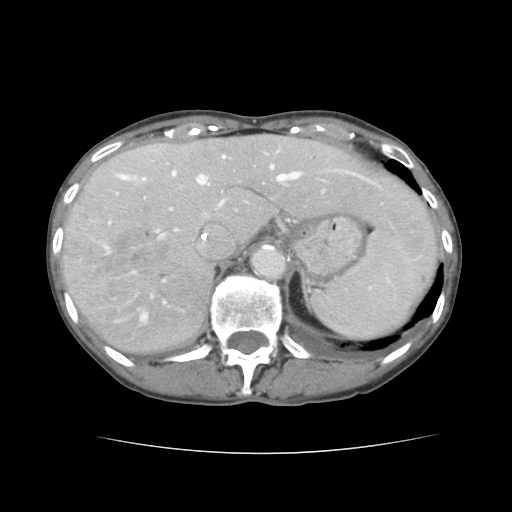
Contrast-enhanced abdominal CT, one axial slice. Slice 105 of 136 in the series (ordered by position). 120 kVp. Intravenous contrast given. Soft-tissue window (W 400 / L 40 HU). 2.5 mm slice thickness. 512 × 512 image matrix, field of view 319 × 319 mm. Female patient, age 77 years. From the clinical record (not read from this slice): diagnosis: colorectal cancer liver metastases, imaged before liver resection; multiple liver metastases: yes; largest metastasis: 3 cm; disease in both lobes: no.
Annotated regions visible in this slice (manually delineated by an expert):
- hepatic veins: box from (x=113, y=156) to (x=380, y=321) px
- liver: (x=63, y=136)–(x=437, y=355)
- planned liver remnant (the part of the liver to remain after resection): (x=161, y=136)–(x=437, y=267)
- portal vein (with intrahepatic branches): (x=109, y=175)–(x=384, y=224)
- liver metastasis: (x=96, y=224)–(x=175, y=284)